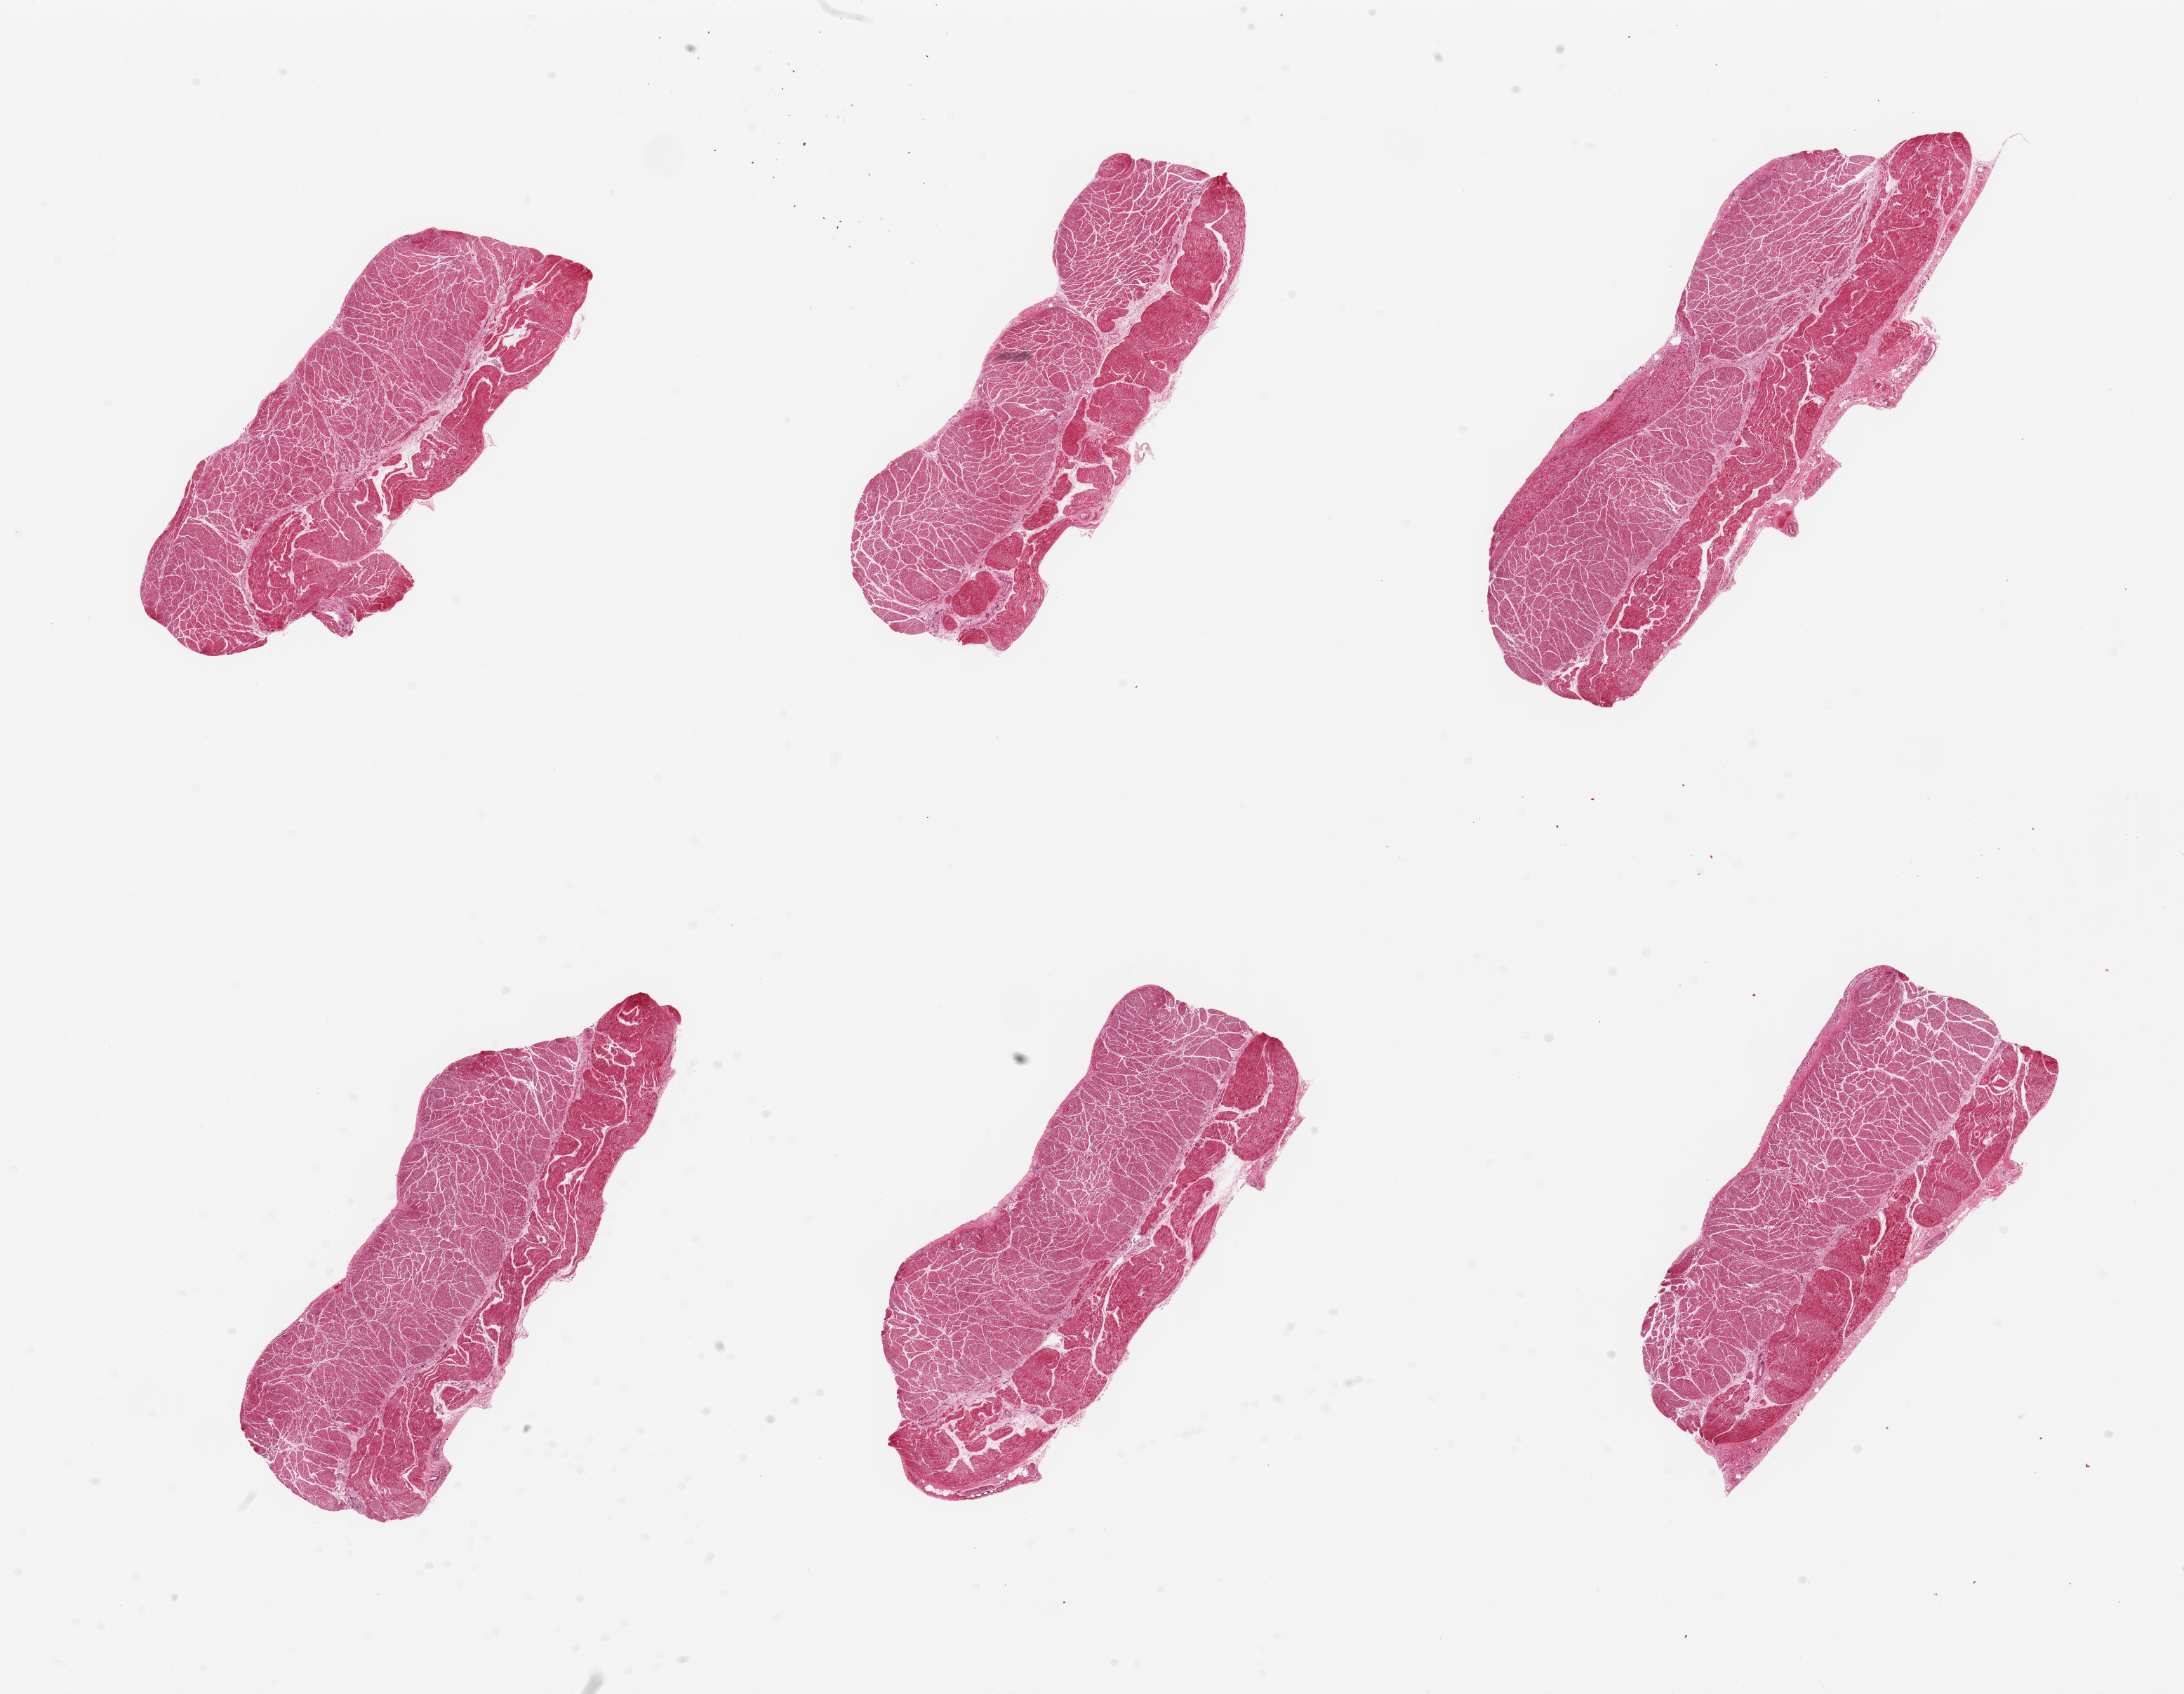
H&E whole-slide image — whole scanned area (about 24.6 x 19.1 mm) shown as a low-resolution overview, PAXgene-fixed paraffin-embedded (PFPE) section, section of esophageal muscle (target tissue), donor tissue sample. Donor: female.
Review note (as recorded): 6 pieces; scattered skeletal muscle fibers in 1 piece <1%.